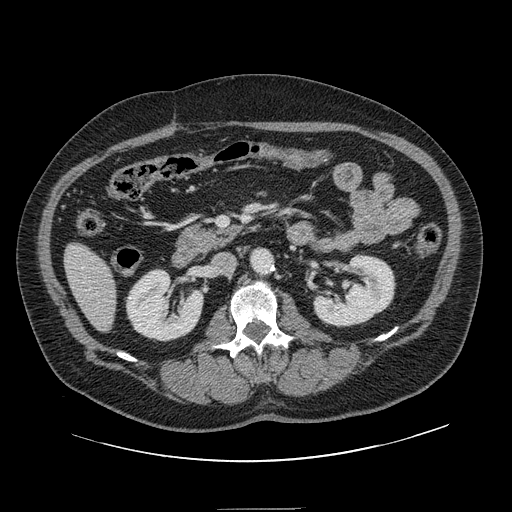
Contrast-enhanced abdominal CT, one axial slice. Slice 45 of 154 in the series (ordered by position). Intravenous contrast given. Soft-tissue window (W 400 / L 40 HU). 2.5 mm slice thickness. 512 × 512 image matrix, field of view 451 × 451 mm. Male patient, age 61 years. Case-level facts recorded for this patient, not image findings: diagnosis: colorectal cancer liver metastases, imaged before liver resection; multiple liver metastases: yes; largest metastasis: 2.6 cm; disease in both lobes: yes.
Annotated regions visible in this slice (outlined manually by an expert reader):
- liver: bounding box [x1, y1, x2, y2] px = [66, 245, 116, 330]
- planned liver remnant (the part of the liver to remain after resection): [66, 245, 116, 330]